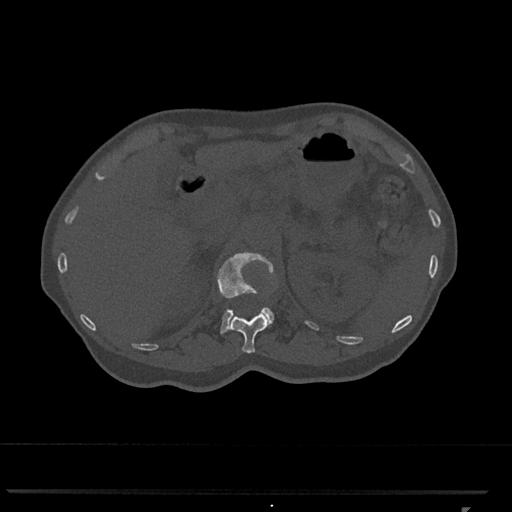
CT including the spine, one axial slice; position 436 of 793 along the scan axis; bone window (W 1800 / L 400 HU); 512 × 512 image matrix. Patient: female, 62 years. From the clinical record (not read from this slice): primary cancer: renal.
Annotated regions visible in this slice (semi-automatically segmented with operator editing):
- L1 vertebra: bounding box <217,252,274,334> (left, top, right, bottom; pixels)
- T12 vertebra: <228,313,270,354>